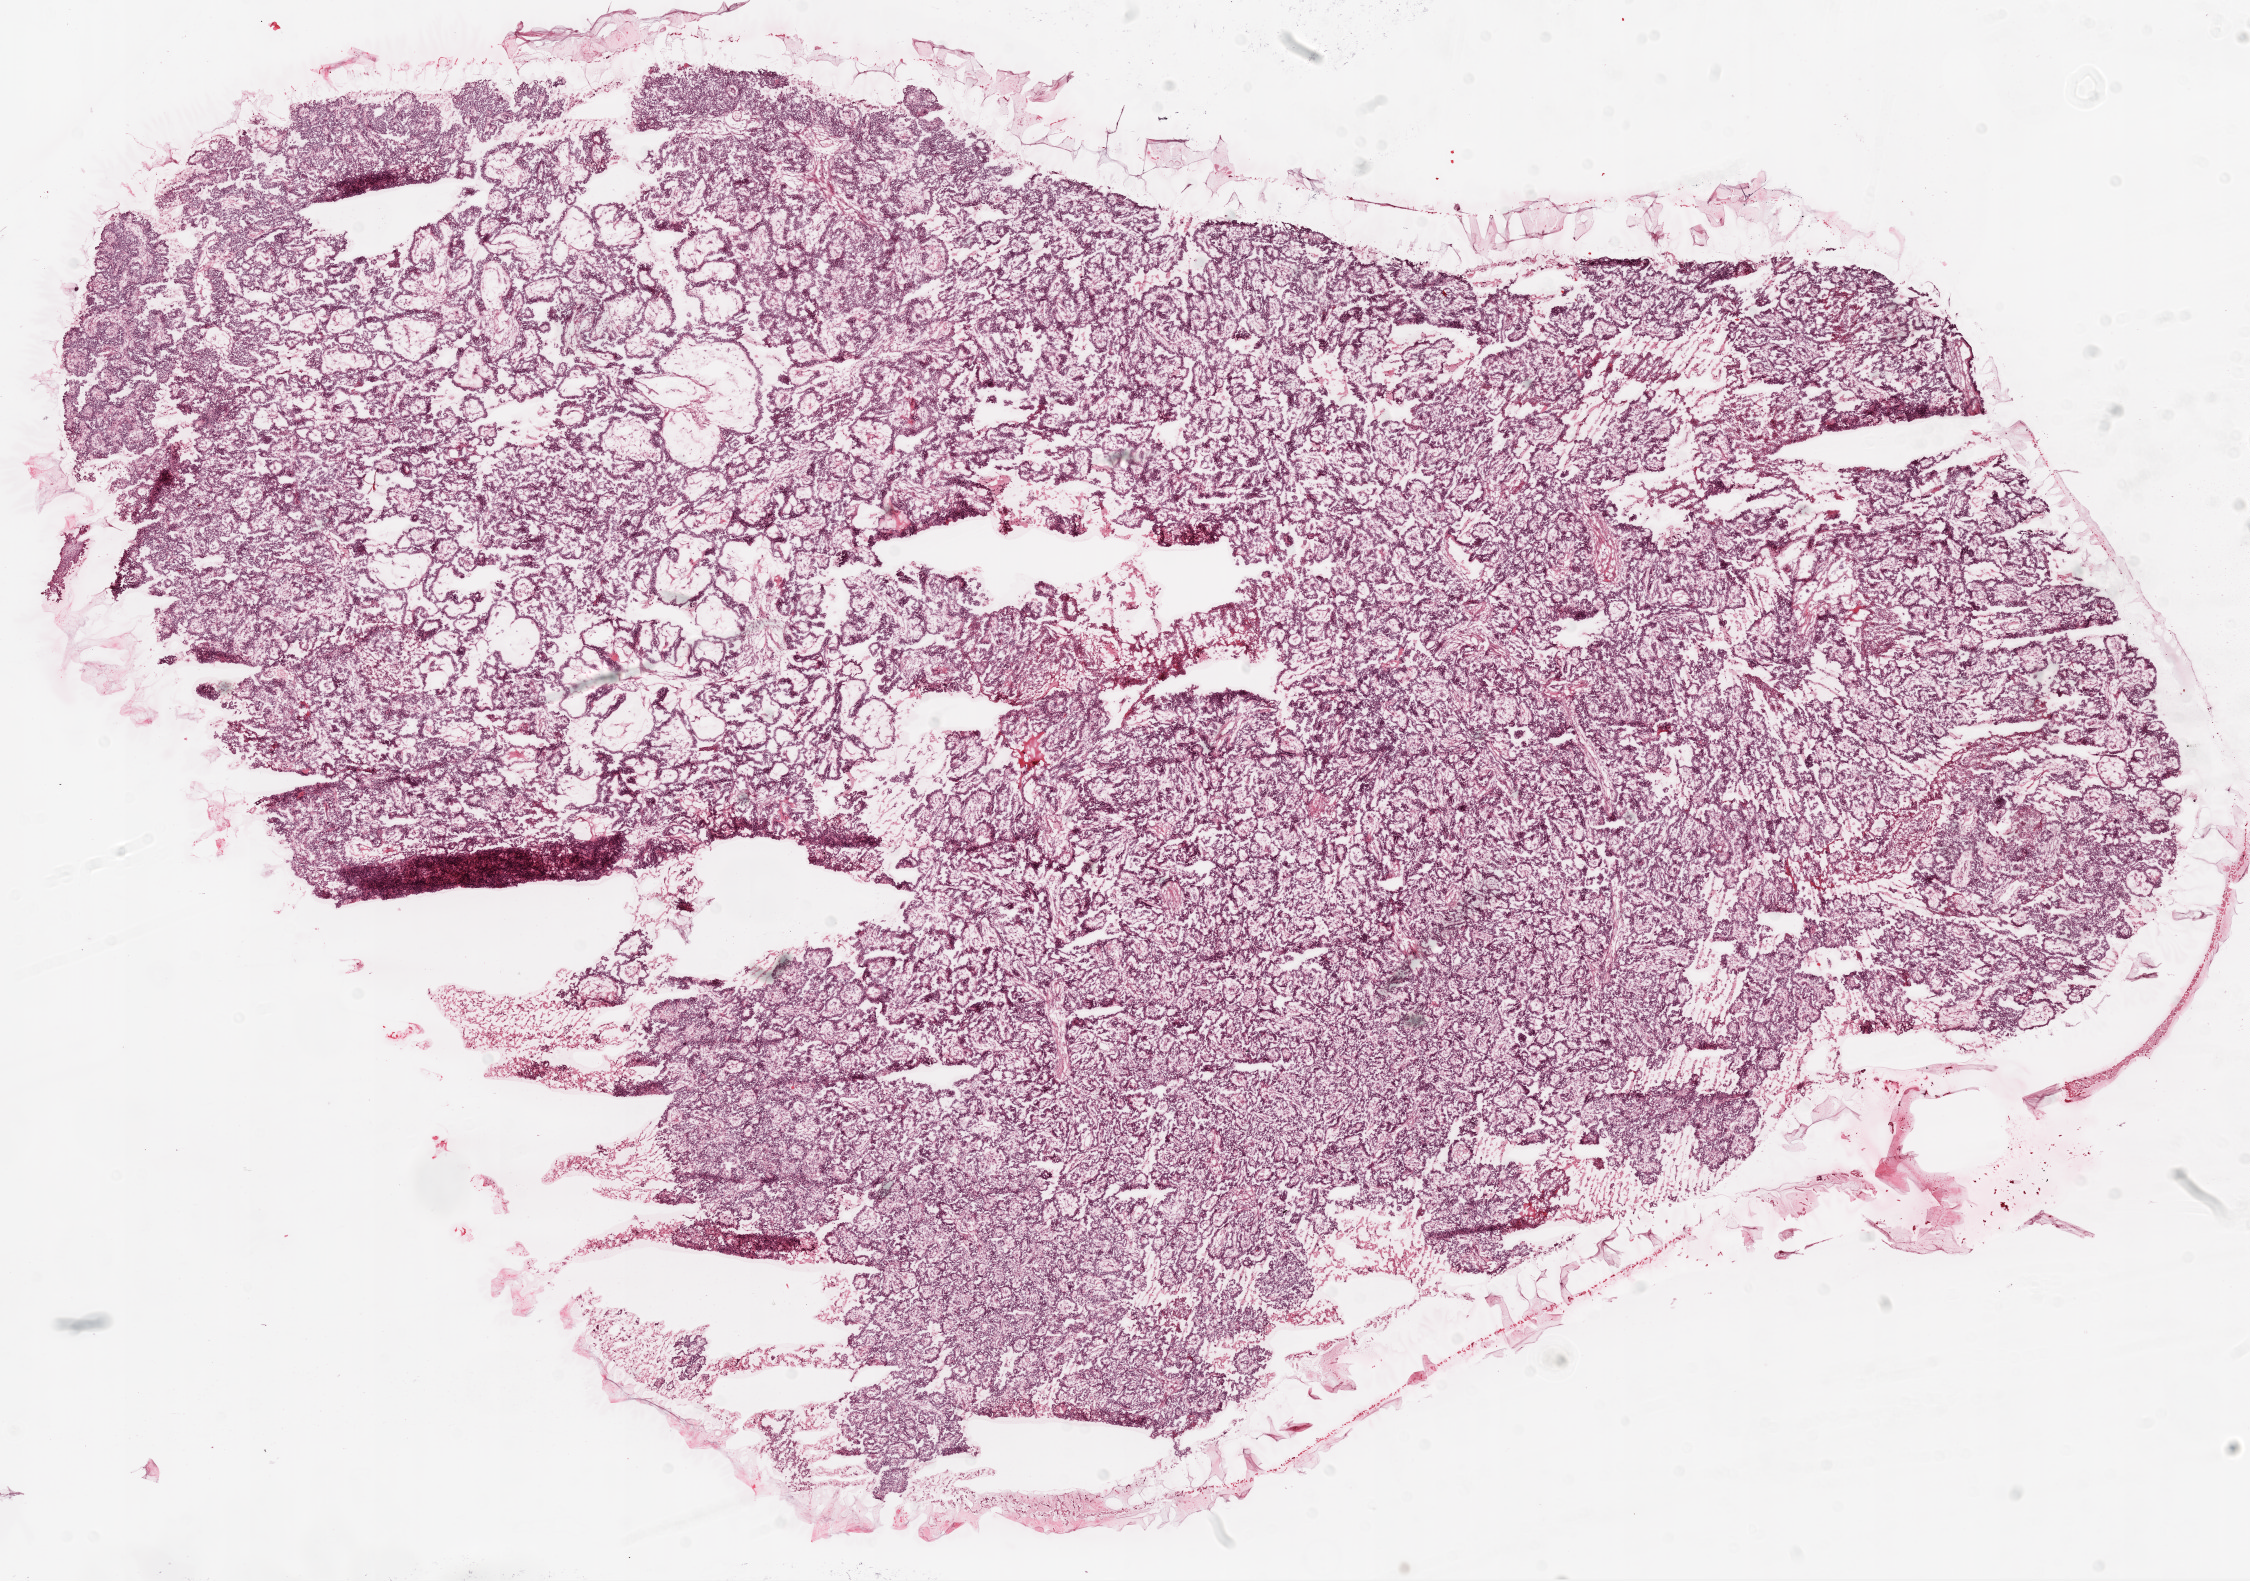
Digitized H&E-stained tissue section (whole slide) — shown as a low-resolution overview of the whole scanned area (about 18.1 x 12.7 mm); frozen section from the top of the tissue portion; sample: primary tumour, ovary. Female patient; age at initial diagnosis 45 years. Histologic grade: G2 (moderately differentiated). Slide review estimates, as recorded: tumour cells 98%, tumour nuclei 90%, normal cells 0%, stromal cells 0%, necrosis 2%.
- FIGO stage: IIIC
- laterality: bilateral
- pathologic diagnosis: Serous cystadenocarcinoma, NOS